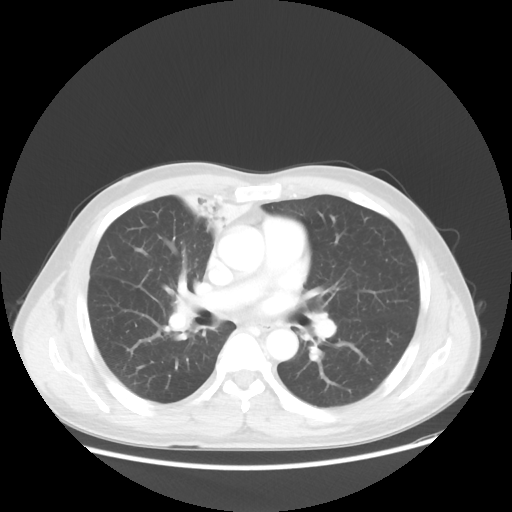
Chest CT, one axial slice; slice 30 of 56 in the series (ordered by position); reconstruction kernel STANDARD; 100 kVp; lung window (W 1500 / L -600 HU); 5 mm slice thickness; 512 × 512 image matrix, field of view 398 × 398 mm. Patient: male, 60 years. From the clinical record (not read from this slice): clinical TNM (as recorded): T2a N1 M0.
Outlined on this slice (bounding box drawn by a radiologist):
- lung tumour (recorded histology: squamous cell carcinoma): bounding box (x1, y1, x2, y2) in pixels: (176, 179, 272, 242)